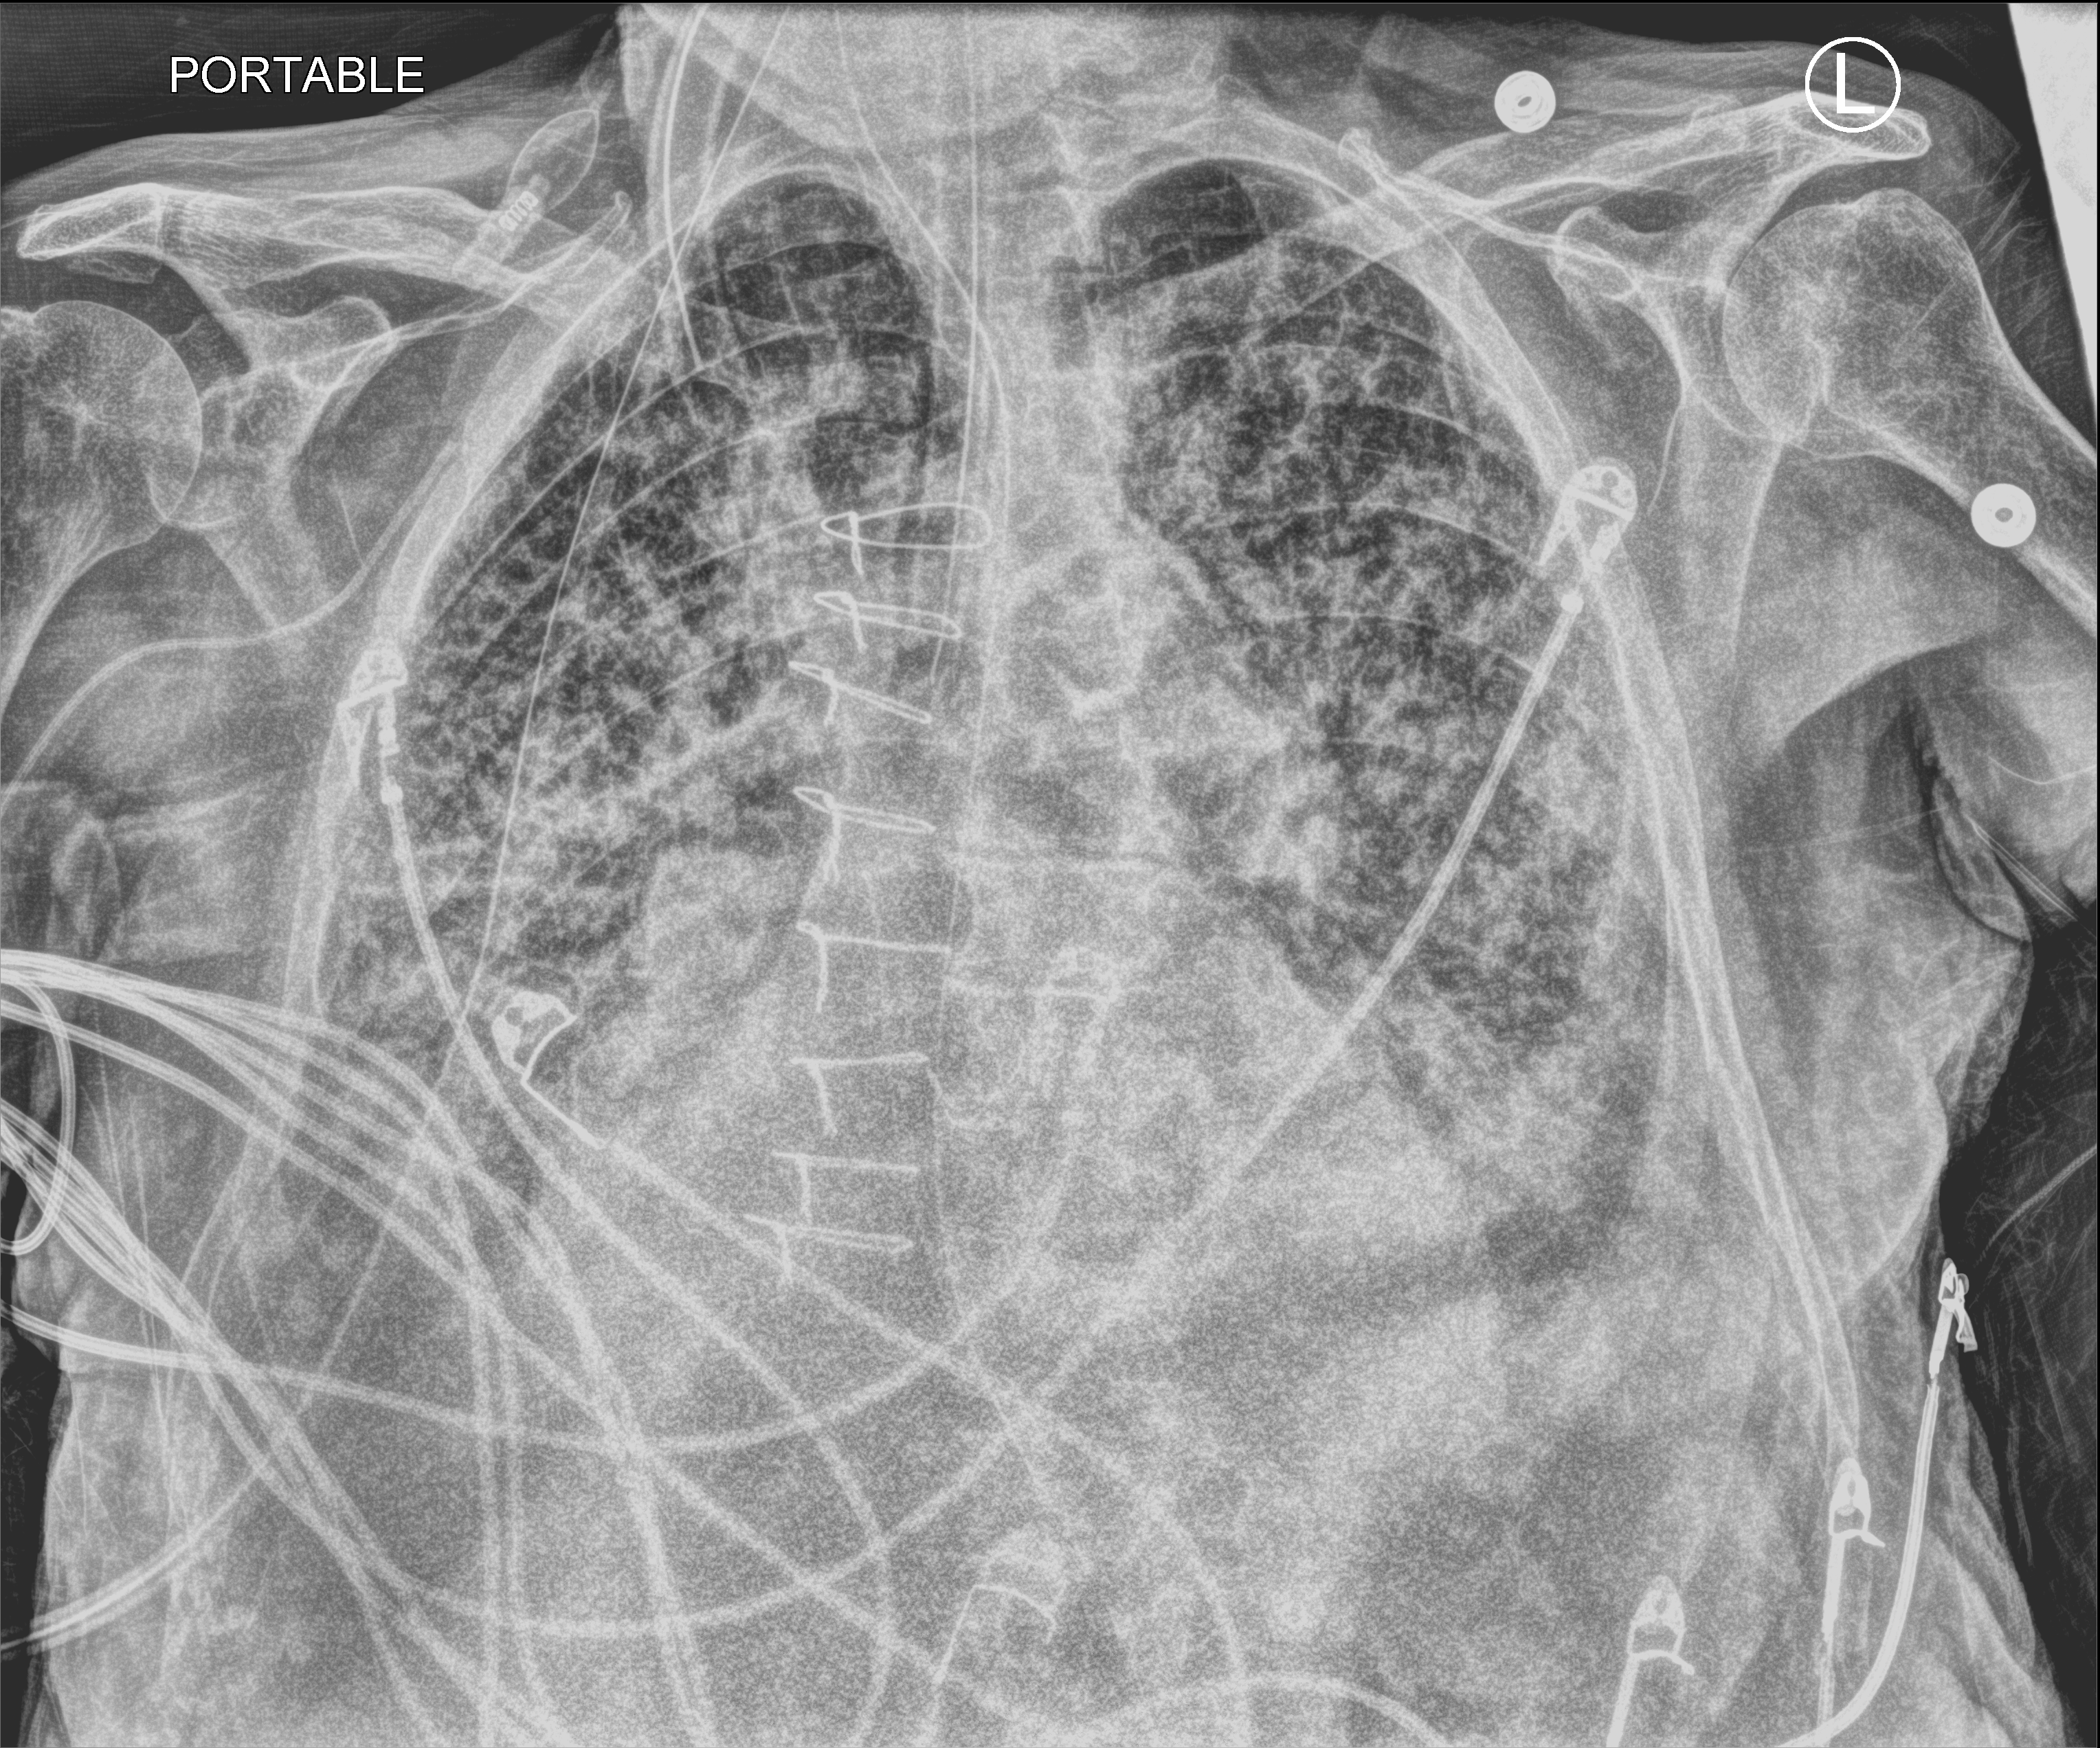
Bedside chest radiograph (computed radiography); anteroposterior (AP) projection. Male patient hospitalised with COVID-19, age 75–90 years.
From the hospital-stay record, not from the radiograph (when in the stay this image was taken is not recorded):
- admitted to intensive care during this hospital stay: yes
- mechanically ventilated during this hospital stay: yes